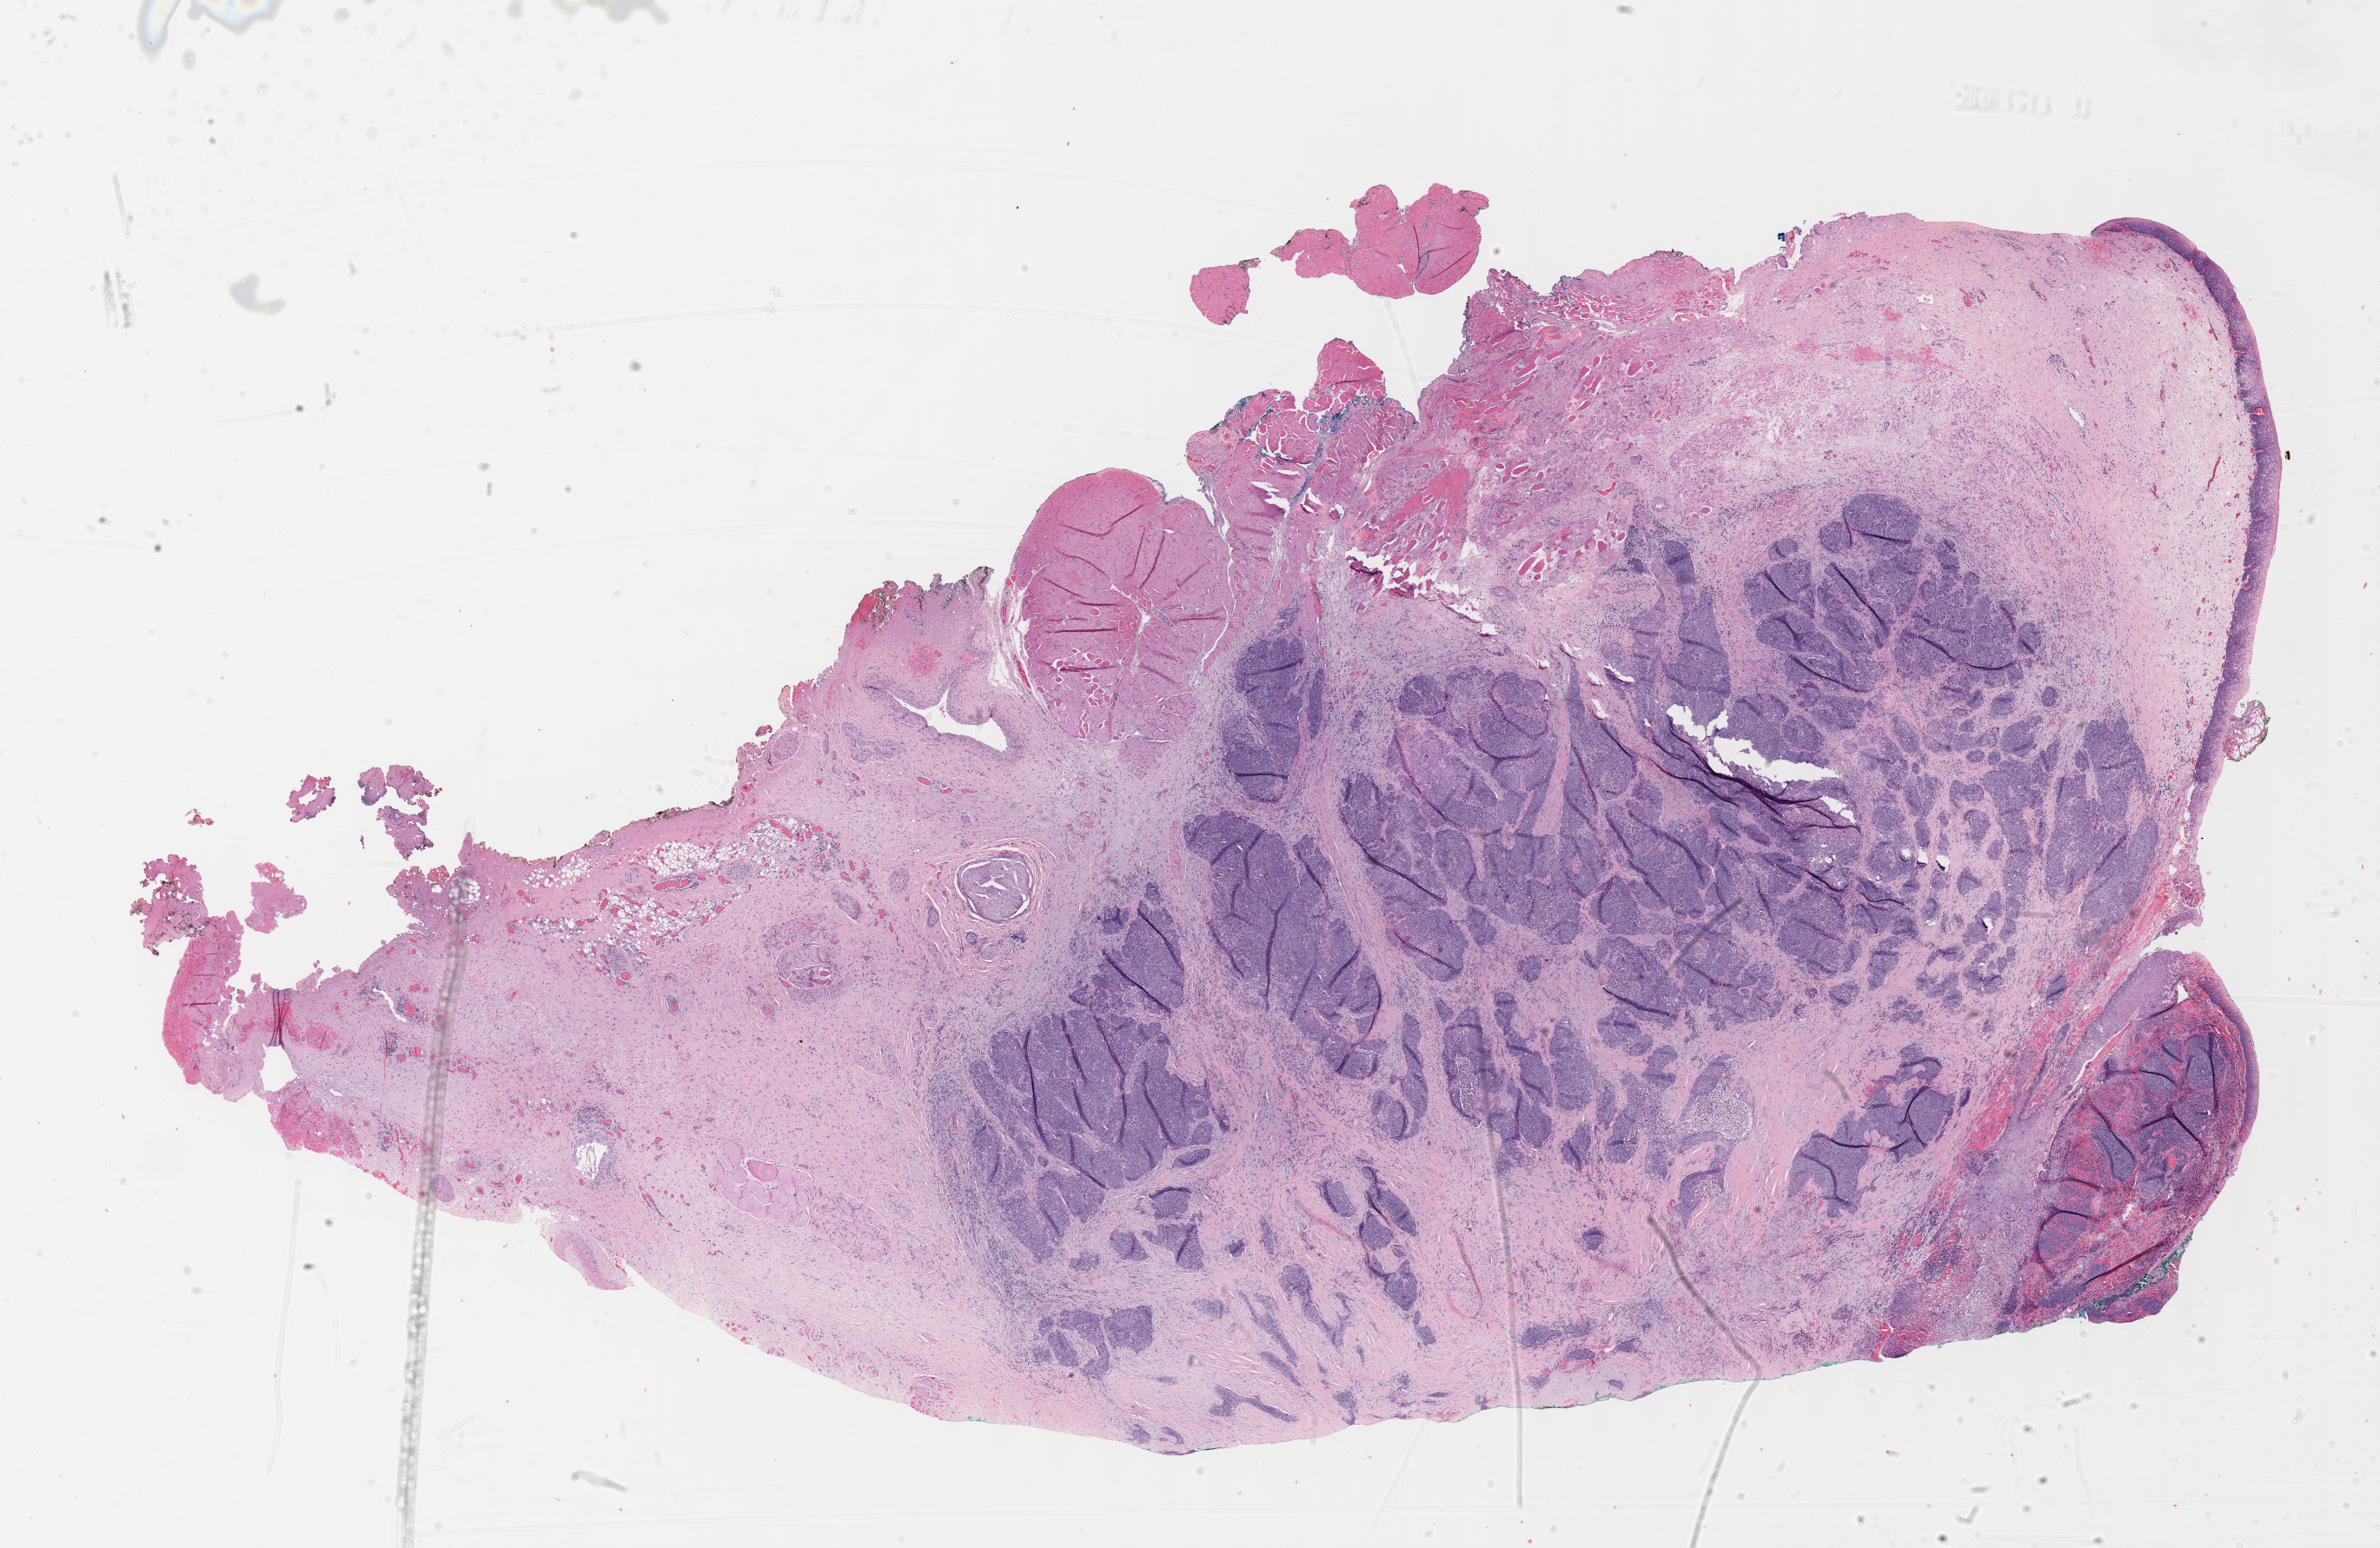
Whole-slide histology image, H&E-stained — low-resolution overview of the scanned area, about 22.1 x 14.4 mm (slide scanned at 40x), formalin-fixed paraffin-embedded (FFPE) diagnostic section, sample: primary tumour, head and neck. Male, age 49 years at initial diagnosis. Histologic grade: GX (grade cannot be assessed).
AJCC pathologic stage: II (7th edition). Histologic diagnosis: Squamous cell carcinoma, NOS.